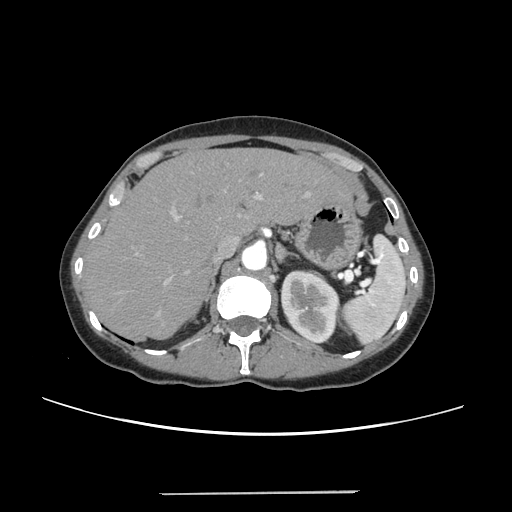
Contrast-enhanced abdominal CT, one axial slice; slice 172 of 240 in the series (ordered by position); intravenous contrast given; soft-tissue window (W 400 / L 40 HU); 1.25 mm slice thickness; 512 × 512 image matrix, field of view 371 × 371 mm. Female patient, age 60 years. Case-level facts recorded for this patient, not image findings: diagnosis: colorectal cancer liver metastases, imaged before liver resection; multiple liver metastases: no; largest metastasis: 1.5 cm; disease in both lobes: no.
Outlined on this slice (manually delineated by an expert):
- liver: bounding box <86,149,349,339> (left, top, right, bottom; pixels)
- planned liver remnant (the part of the liver to remain after resection): <86,149,348,339>
- portal vein (with intrahepatic branches): <136,174,309,285>